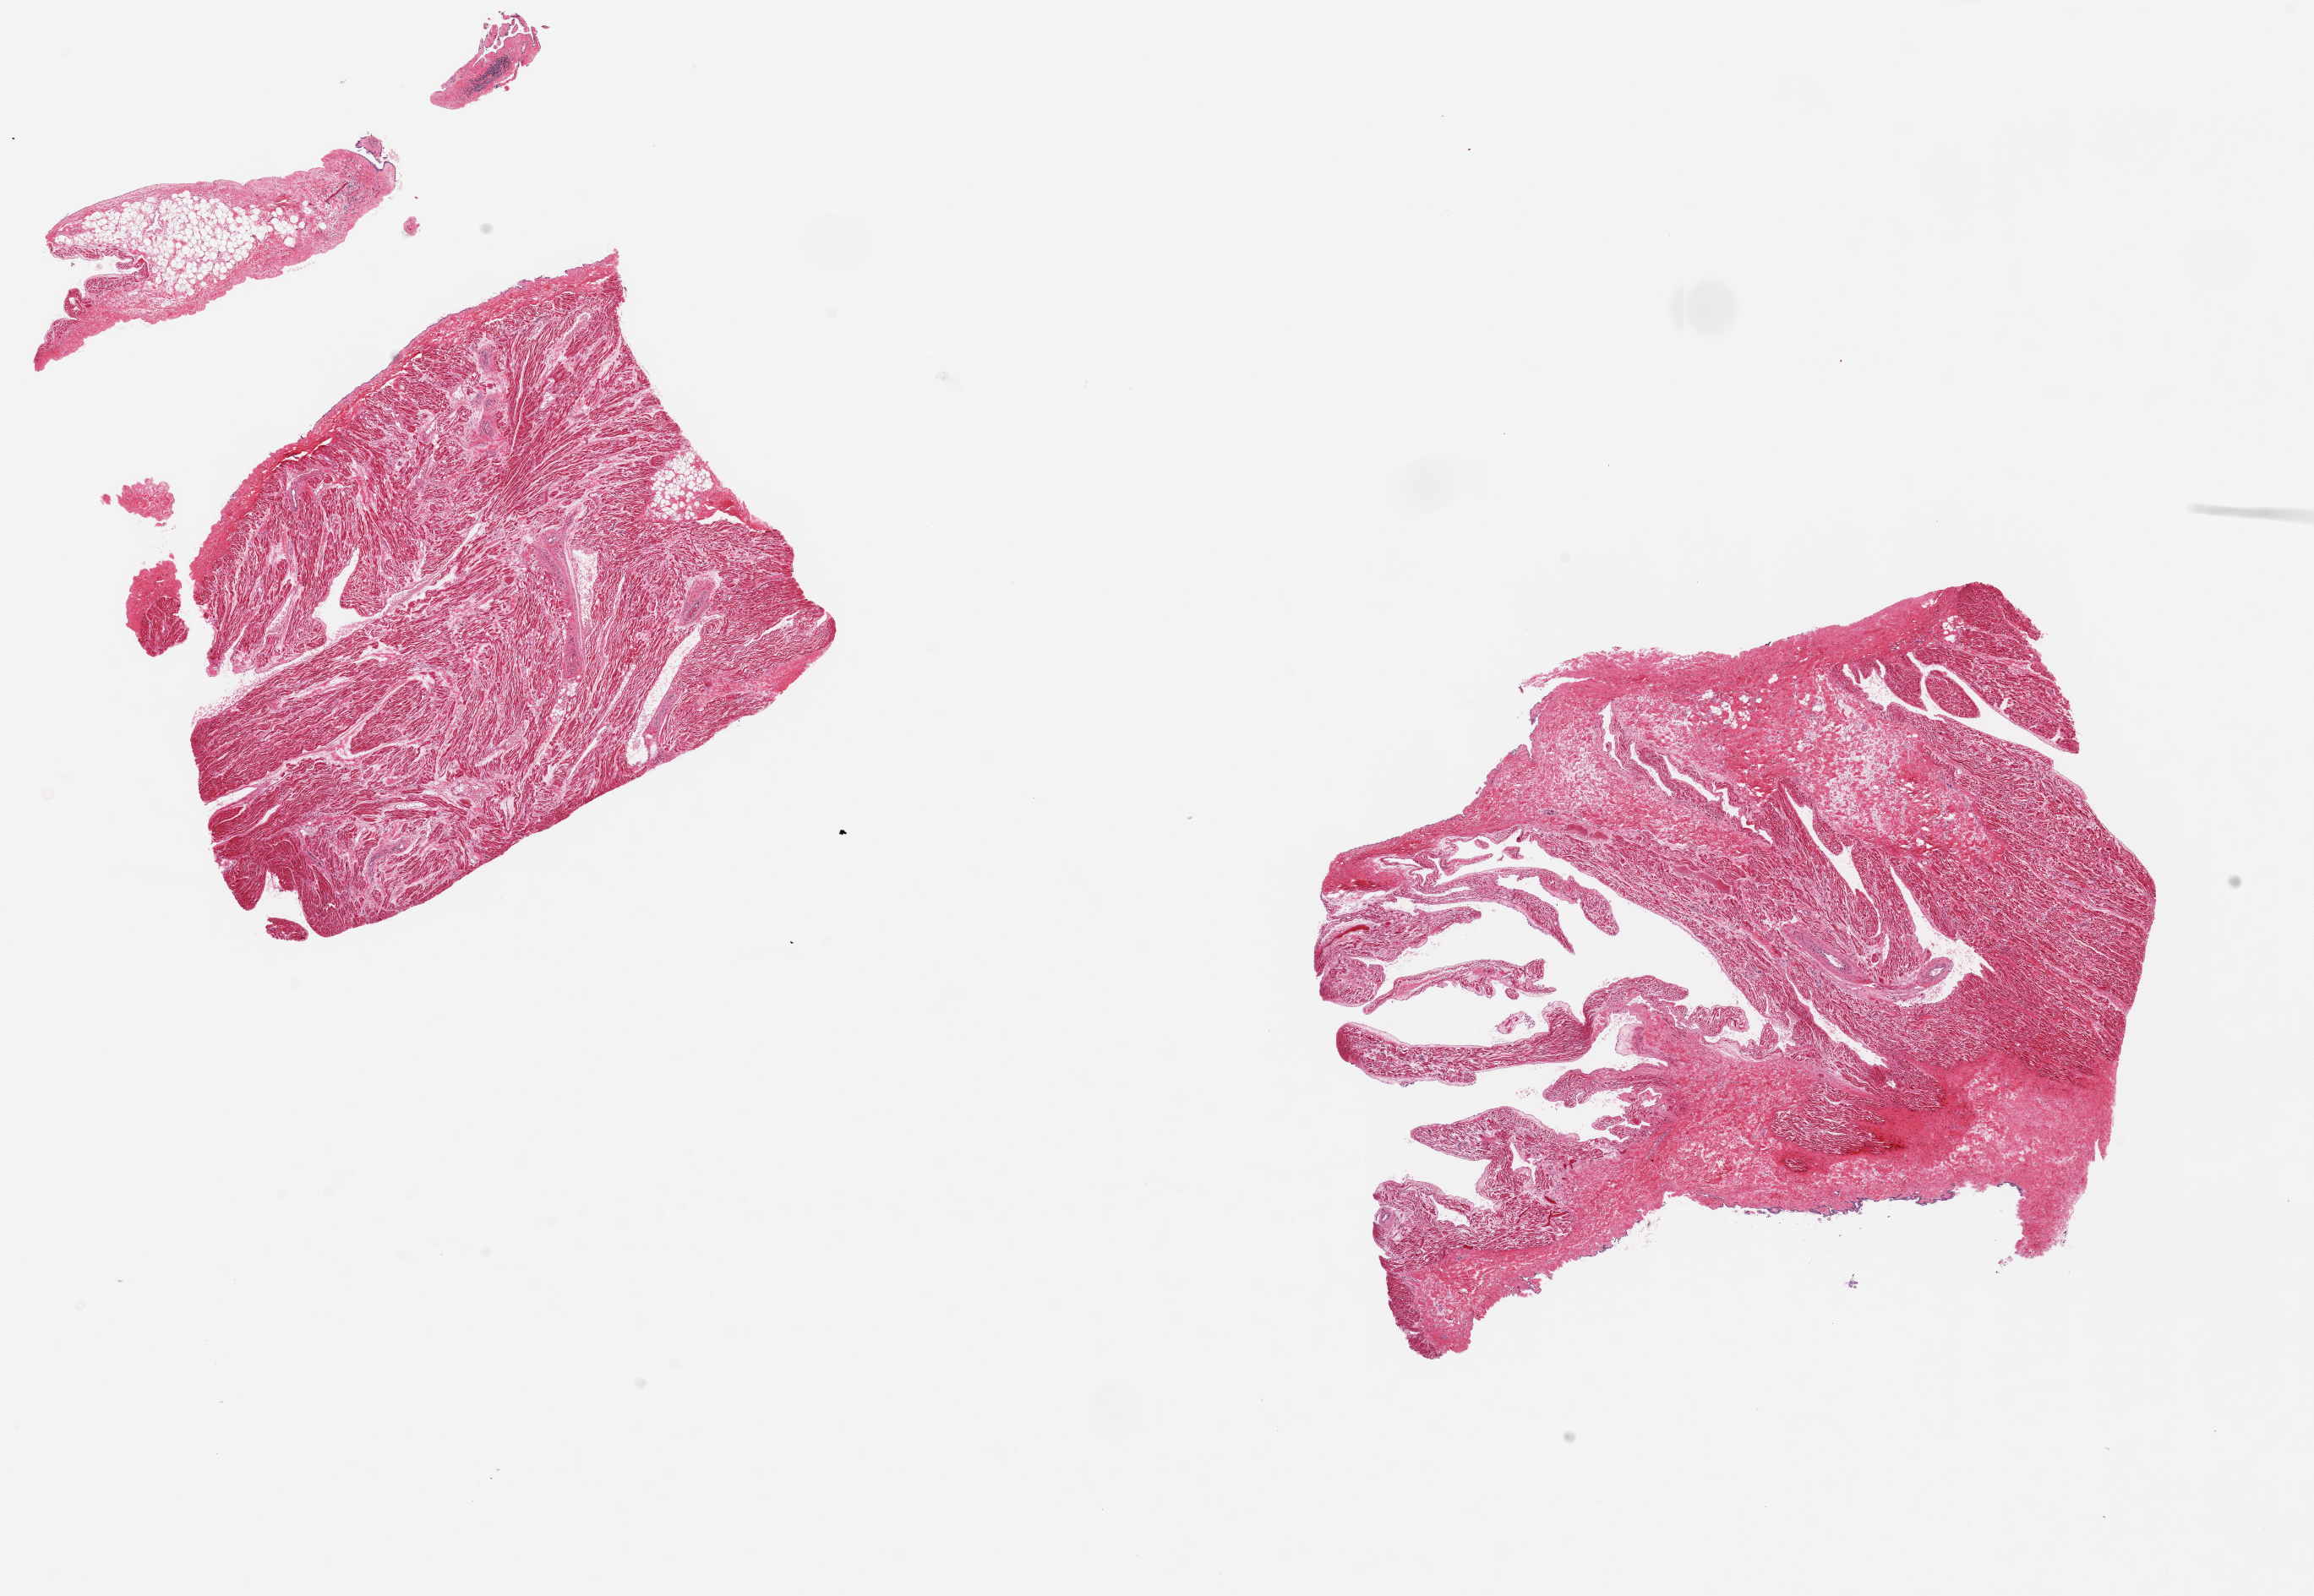
Whole-slide image, H&E stain, brightfield — shown as a low-resolution overview of the whole scanned area (about 21.7 x 14.9 mm); PAXgene-fixed, paraffin-embedded tissue; section of auricular appendage (target tissue); tissue donor sample. Donor sex: male.
- review note (as recorded): 2 pieces ~7x6mm